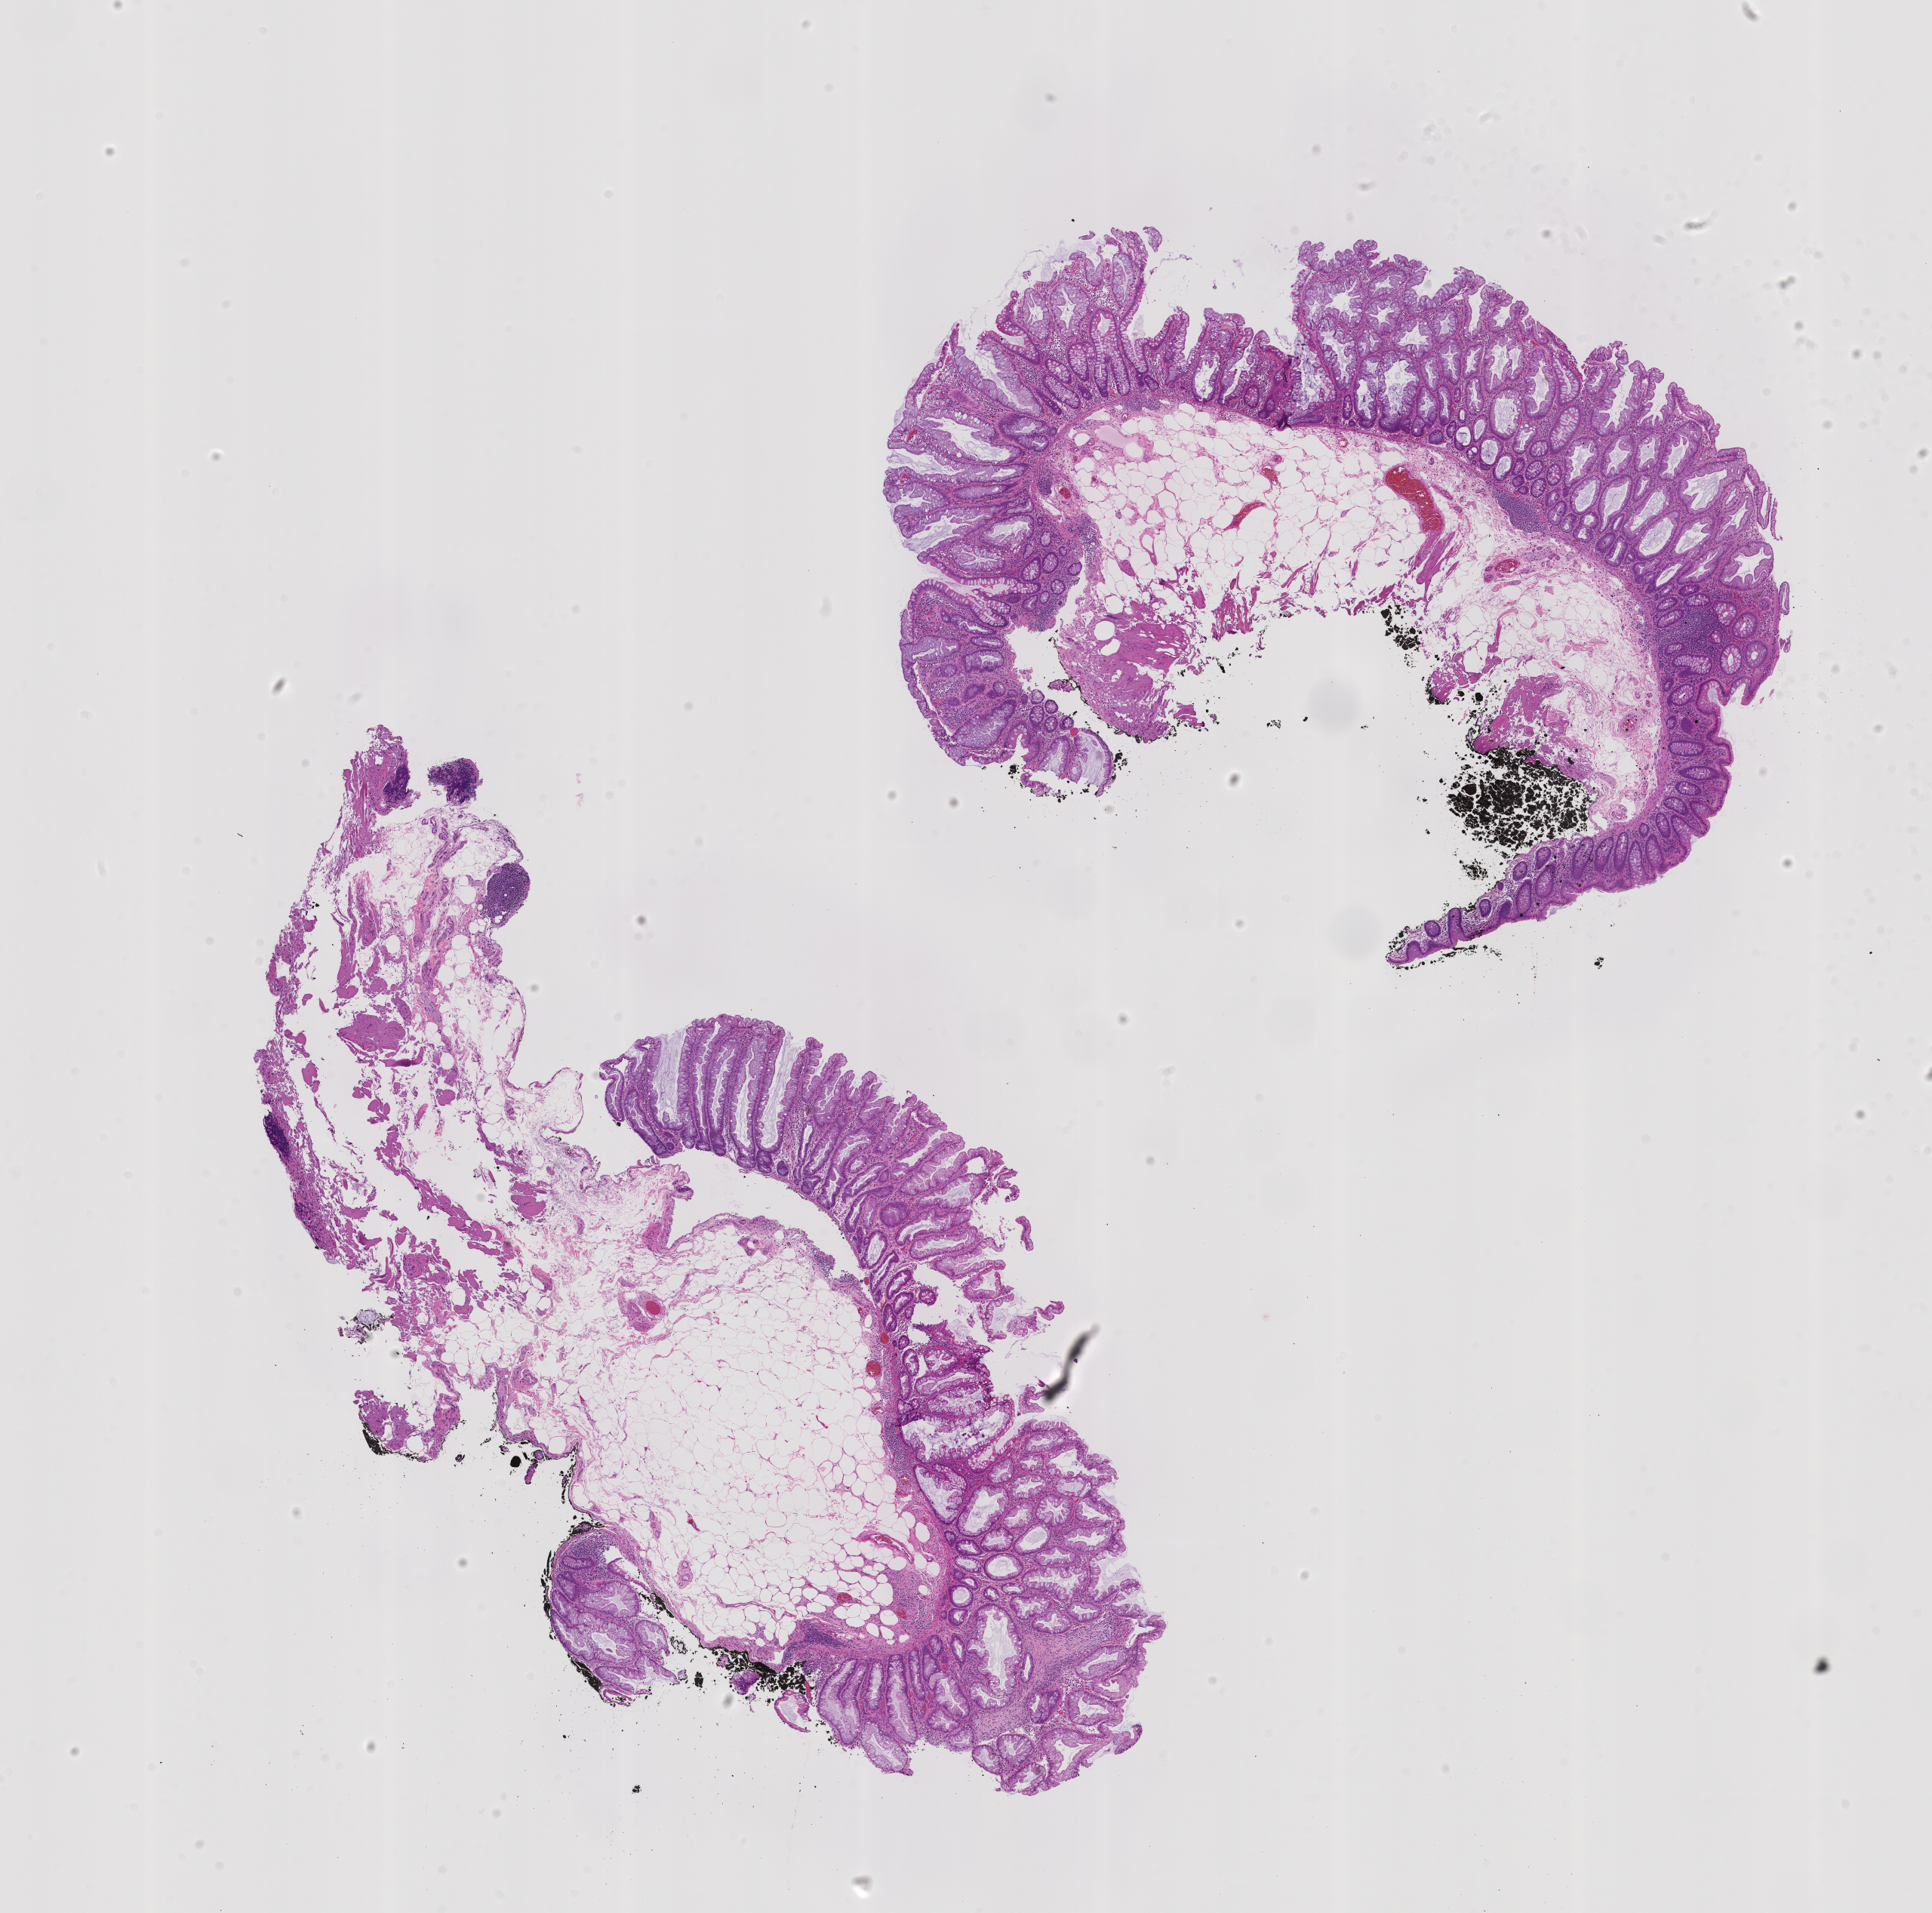
Haematoxylin and eosin whole-slide image of a colon biopsy, shown as a low-resolution overview of the whole scanned area (about 10.2 x 10.1 mm). Formalin-fixed paraffin-embedded section. Ascending colon. Patient: female.
Lesion category (as recorded): premalignant.